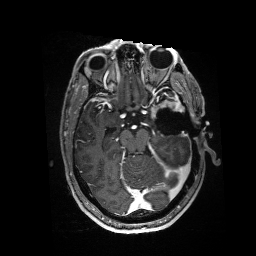
Brain MRI from a brain-tumour surgery series, one axial slice; T1-weighted post-contrast; 1 mm slice thickness; 256 × 256 image matrix, field of view 256 × 256 mm. Case-level facts recorded for this patient, not image findings: histopathology: Glioblastoma; WHO grade: 4; IDH mutation: no.
Structures marked on this image (manually delineated by an expert):
- residual tumour: bounding box <151,96,185,118> (left, top, right, bottom; pixels)